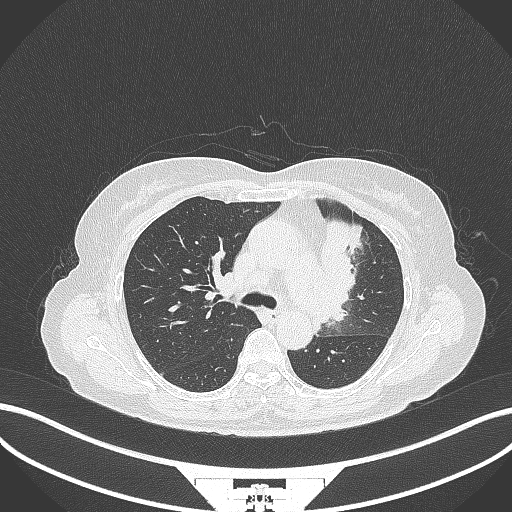
Chest CT, one axial slice. Slice 219 of 382 in the series (ordered by position). 120 kVp. Lung window (W 1500 / L -600 HU). 1 mm slice thickness. 512 × 512 image matrix, field of view 400 × 400 mm. Patient: female, 64 years. Case-level facts recorded for this patient, not image findings: clinical TNM (as recorded): T2a N2 M0.
Annotated regions visible in this slice (bounding box drawn by a radiologist):
- lung tumour (recorded histology: adenocarcinoma): bounding box <314,216,363,329> (left, top, right, bottom; pixels)